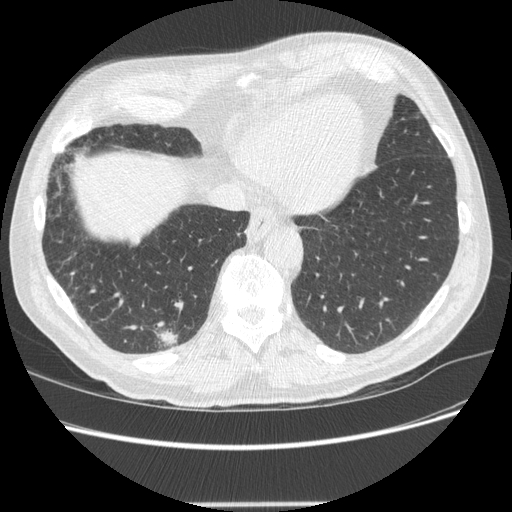
Low-dose screening chest CT, one axial slice. Position 59 of 245 along the scan axis. Reconstruction kernel STANDARD. 120 kVp. Lung window (W 1500 / L -600 HU). 512 × 512 image matrix.
Structures marked on this image (manually delineated by an expert):
- lesion 1 (tumor, lower lobe of right lung): box from (x=159, y=330) to (x=178, y=346) px